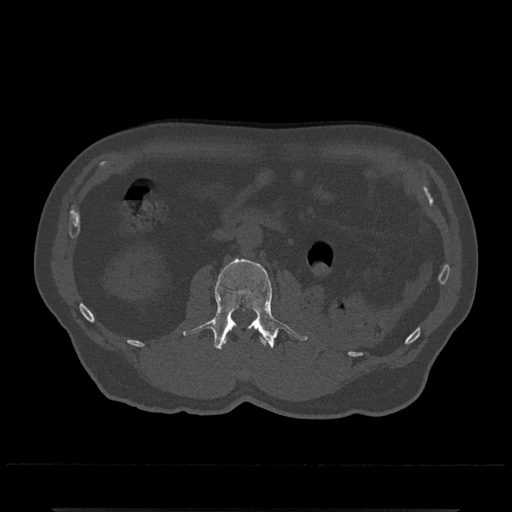
CT including the spine, one axial slice; reconstruction kernel Br40s/3; 120 kVp; bone window (W 1800 / L 400 HU); 512 × 512 image matrix, field of view 393 × 393 mm. Patient: male, 67 years. From the clinical record (not read from this slice): primary cancer: prostate.
Outlined on this slice (semi-automatically segmented with operator editing):
- L1 vertebra: bounding box [x1, y1, x2, y2] px = [224, 337, 267, 346]
- L2 vertebra: [183, 258, 308, 350]